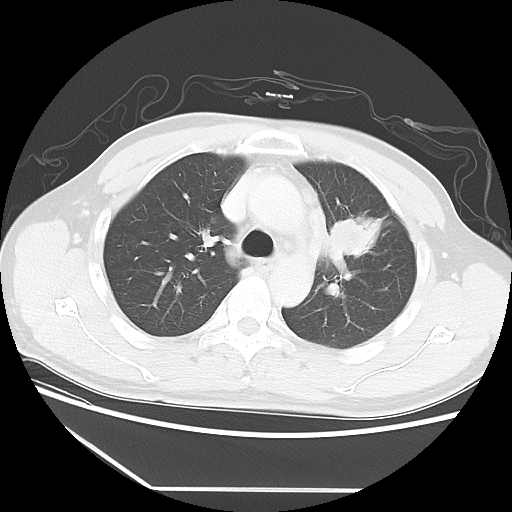
Chest CT, one axial slice. Position 39 of 56 along the scan axis. Lung window (W 1500 / L -600 HU). 5 mm slice thickness. 512 × 512 image matrix, field of view 373 × 373 mm. Patient: male, 53 years. Case-level facts recorded for this patient, not image findings: clinical TNM (as recorded): T2a N1 M1b.
Outlined on this slice (rectangle marked by the reading radiologist):
- lung tumour (recorded histology: adenocarcinoma): box from (x=328, y=210) to (x=384, y=264) px